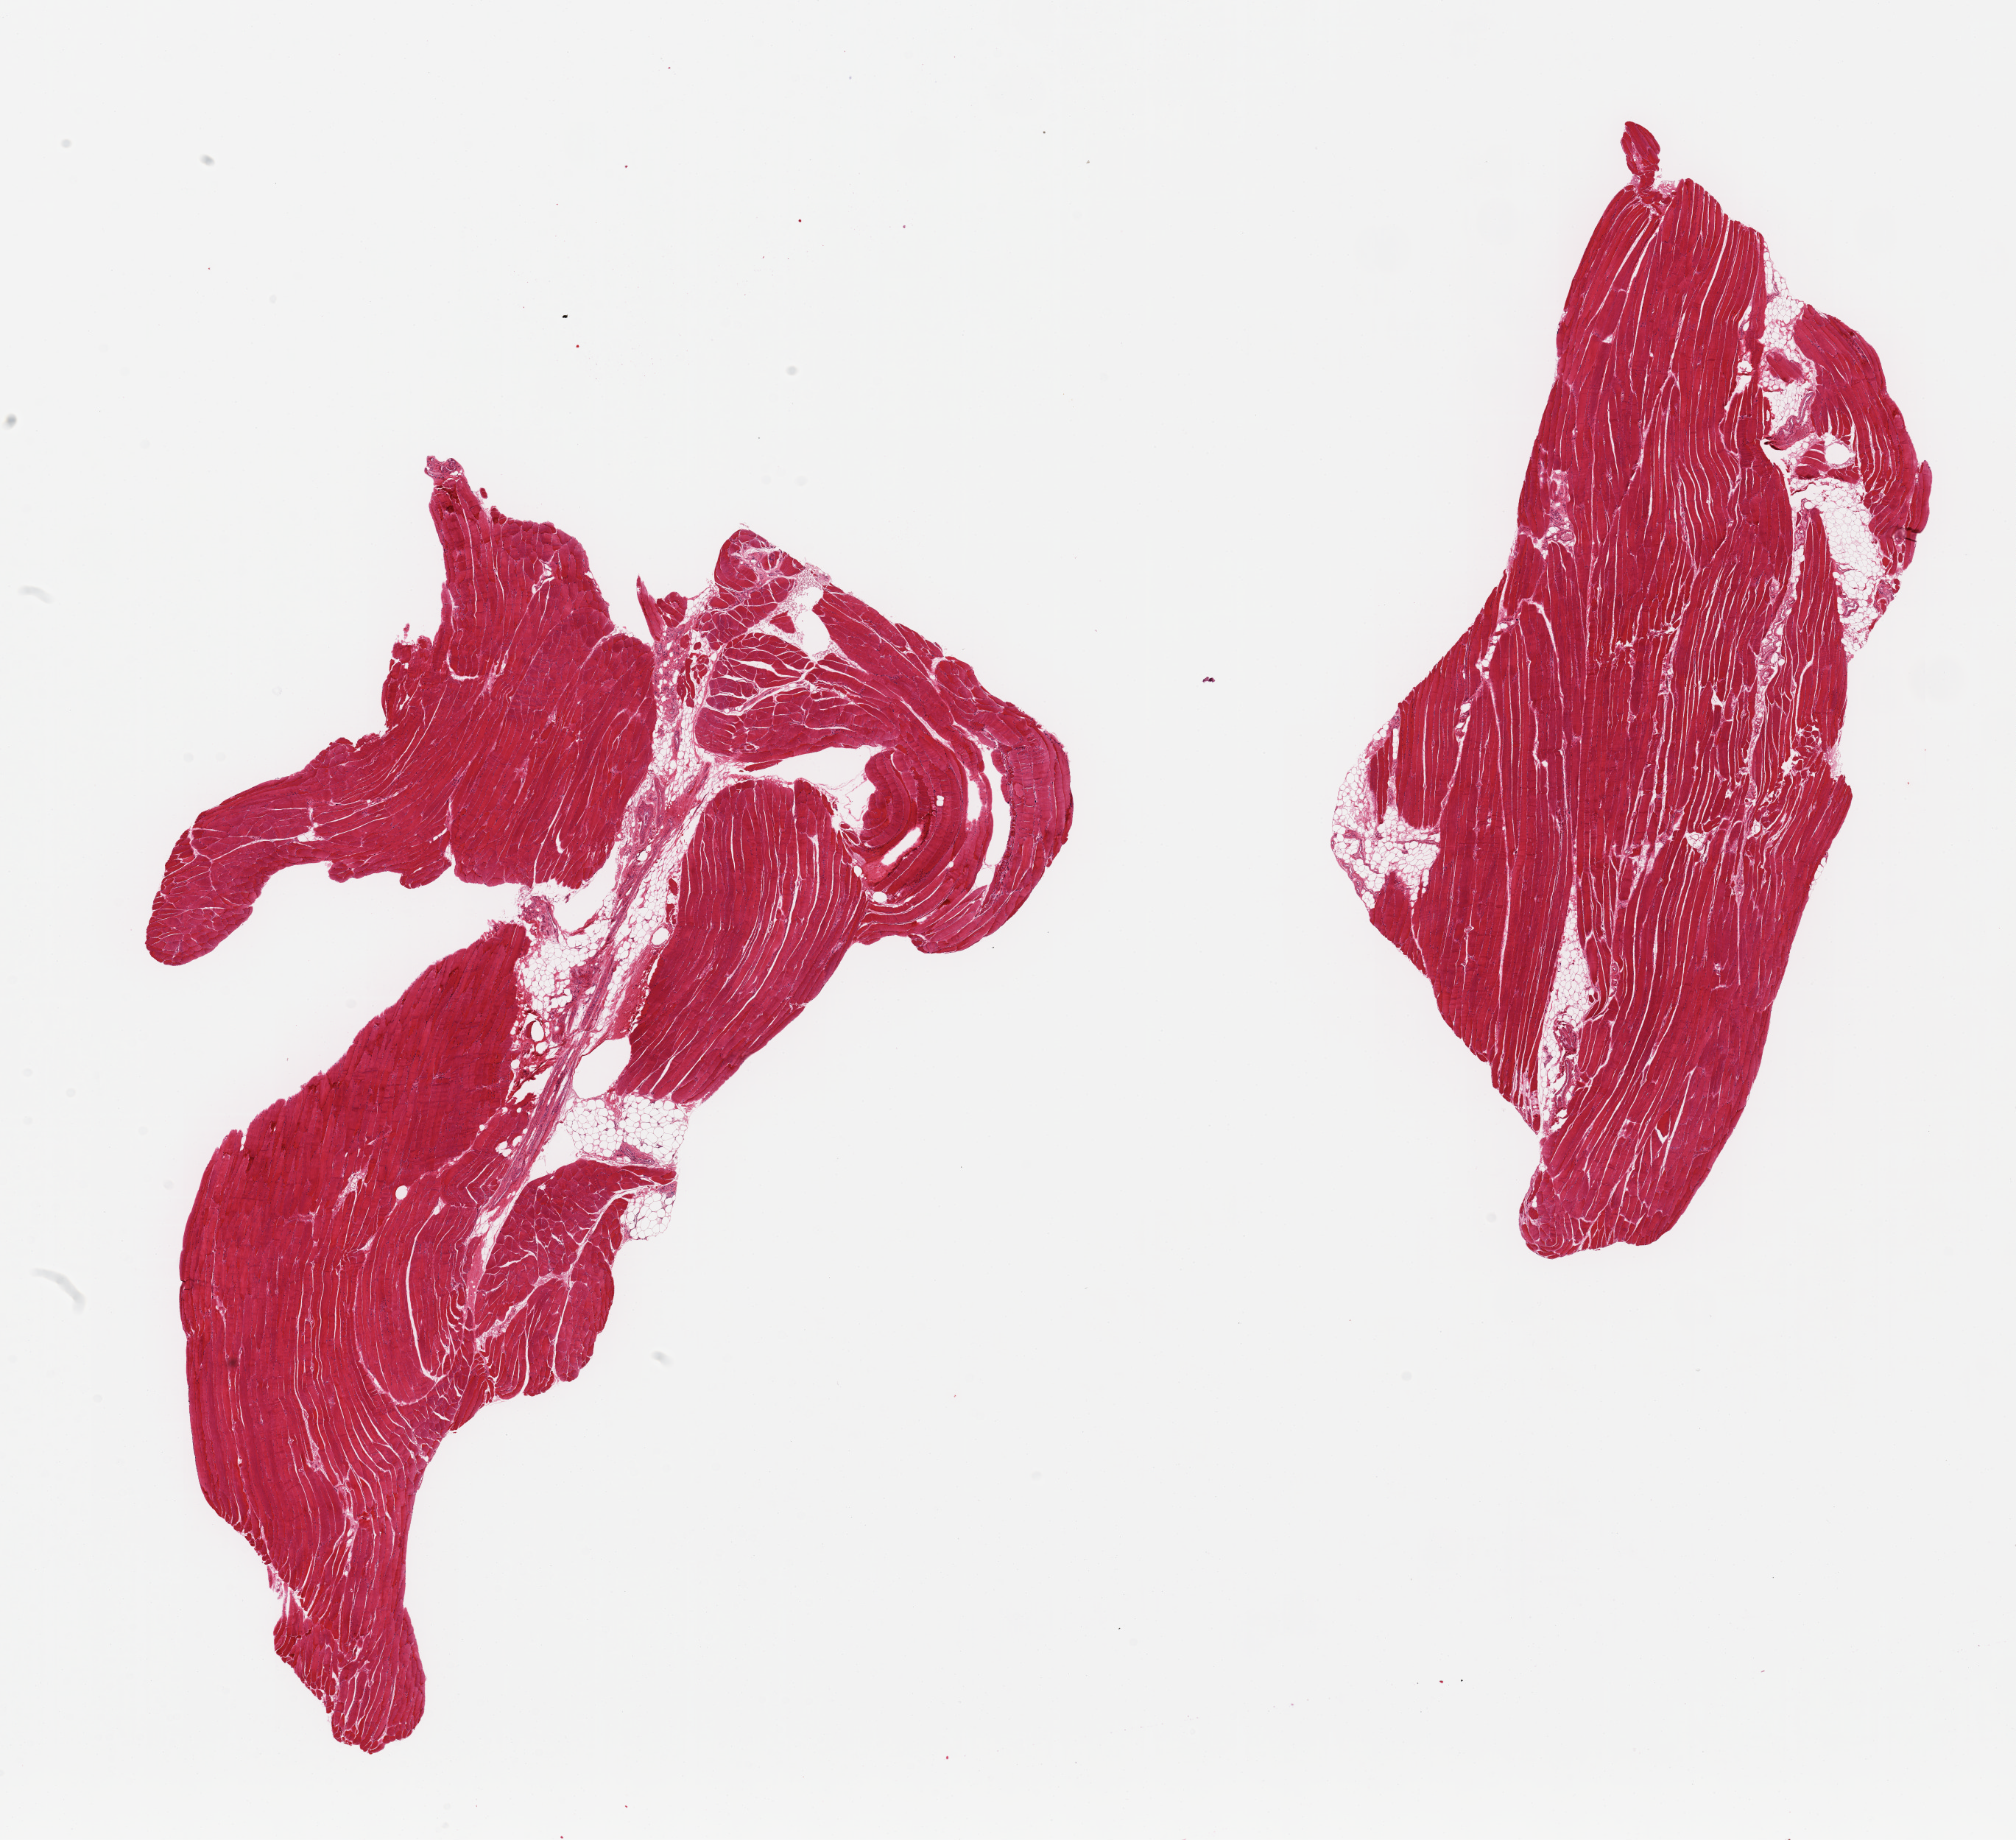
H&E whole-slide image, shown as a low-resolution overview of the whole scanned area (about 21.7 x 19.8 mm), PAXgene-fixed paraffin-embedded (PFPE) section, target tissue: skeletal muscle, tissue donor sample. Female donor.
- pathologist's review note for this sample: 2 pieces; 5% internal fat